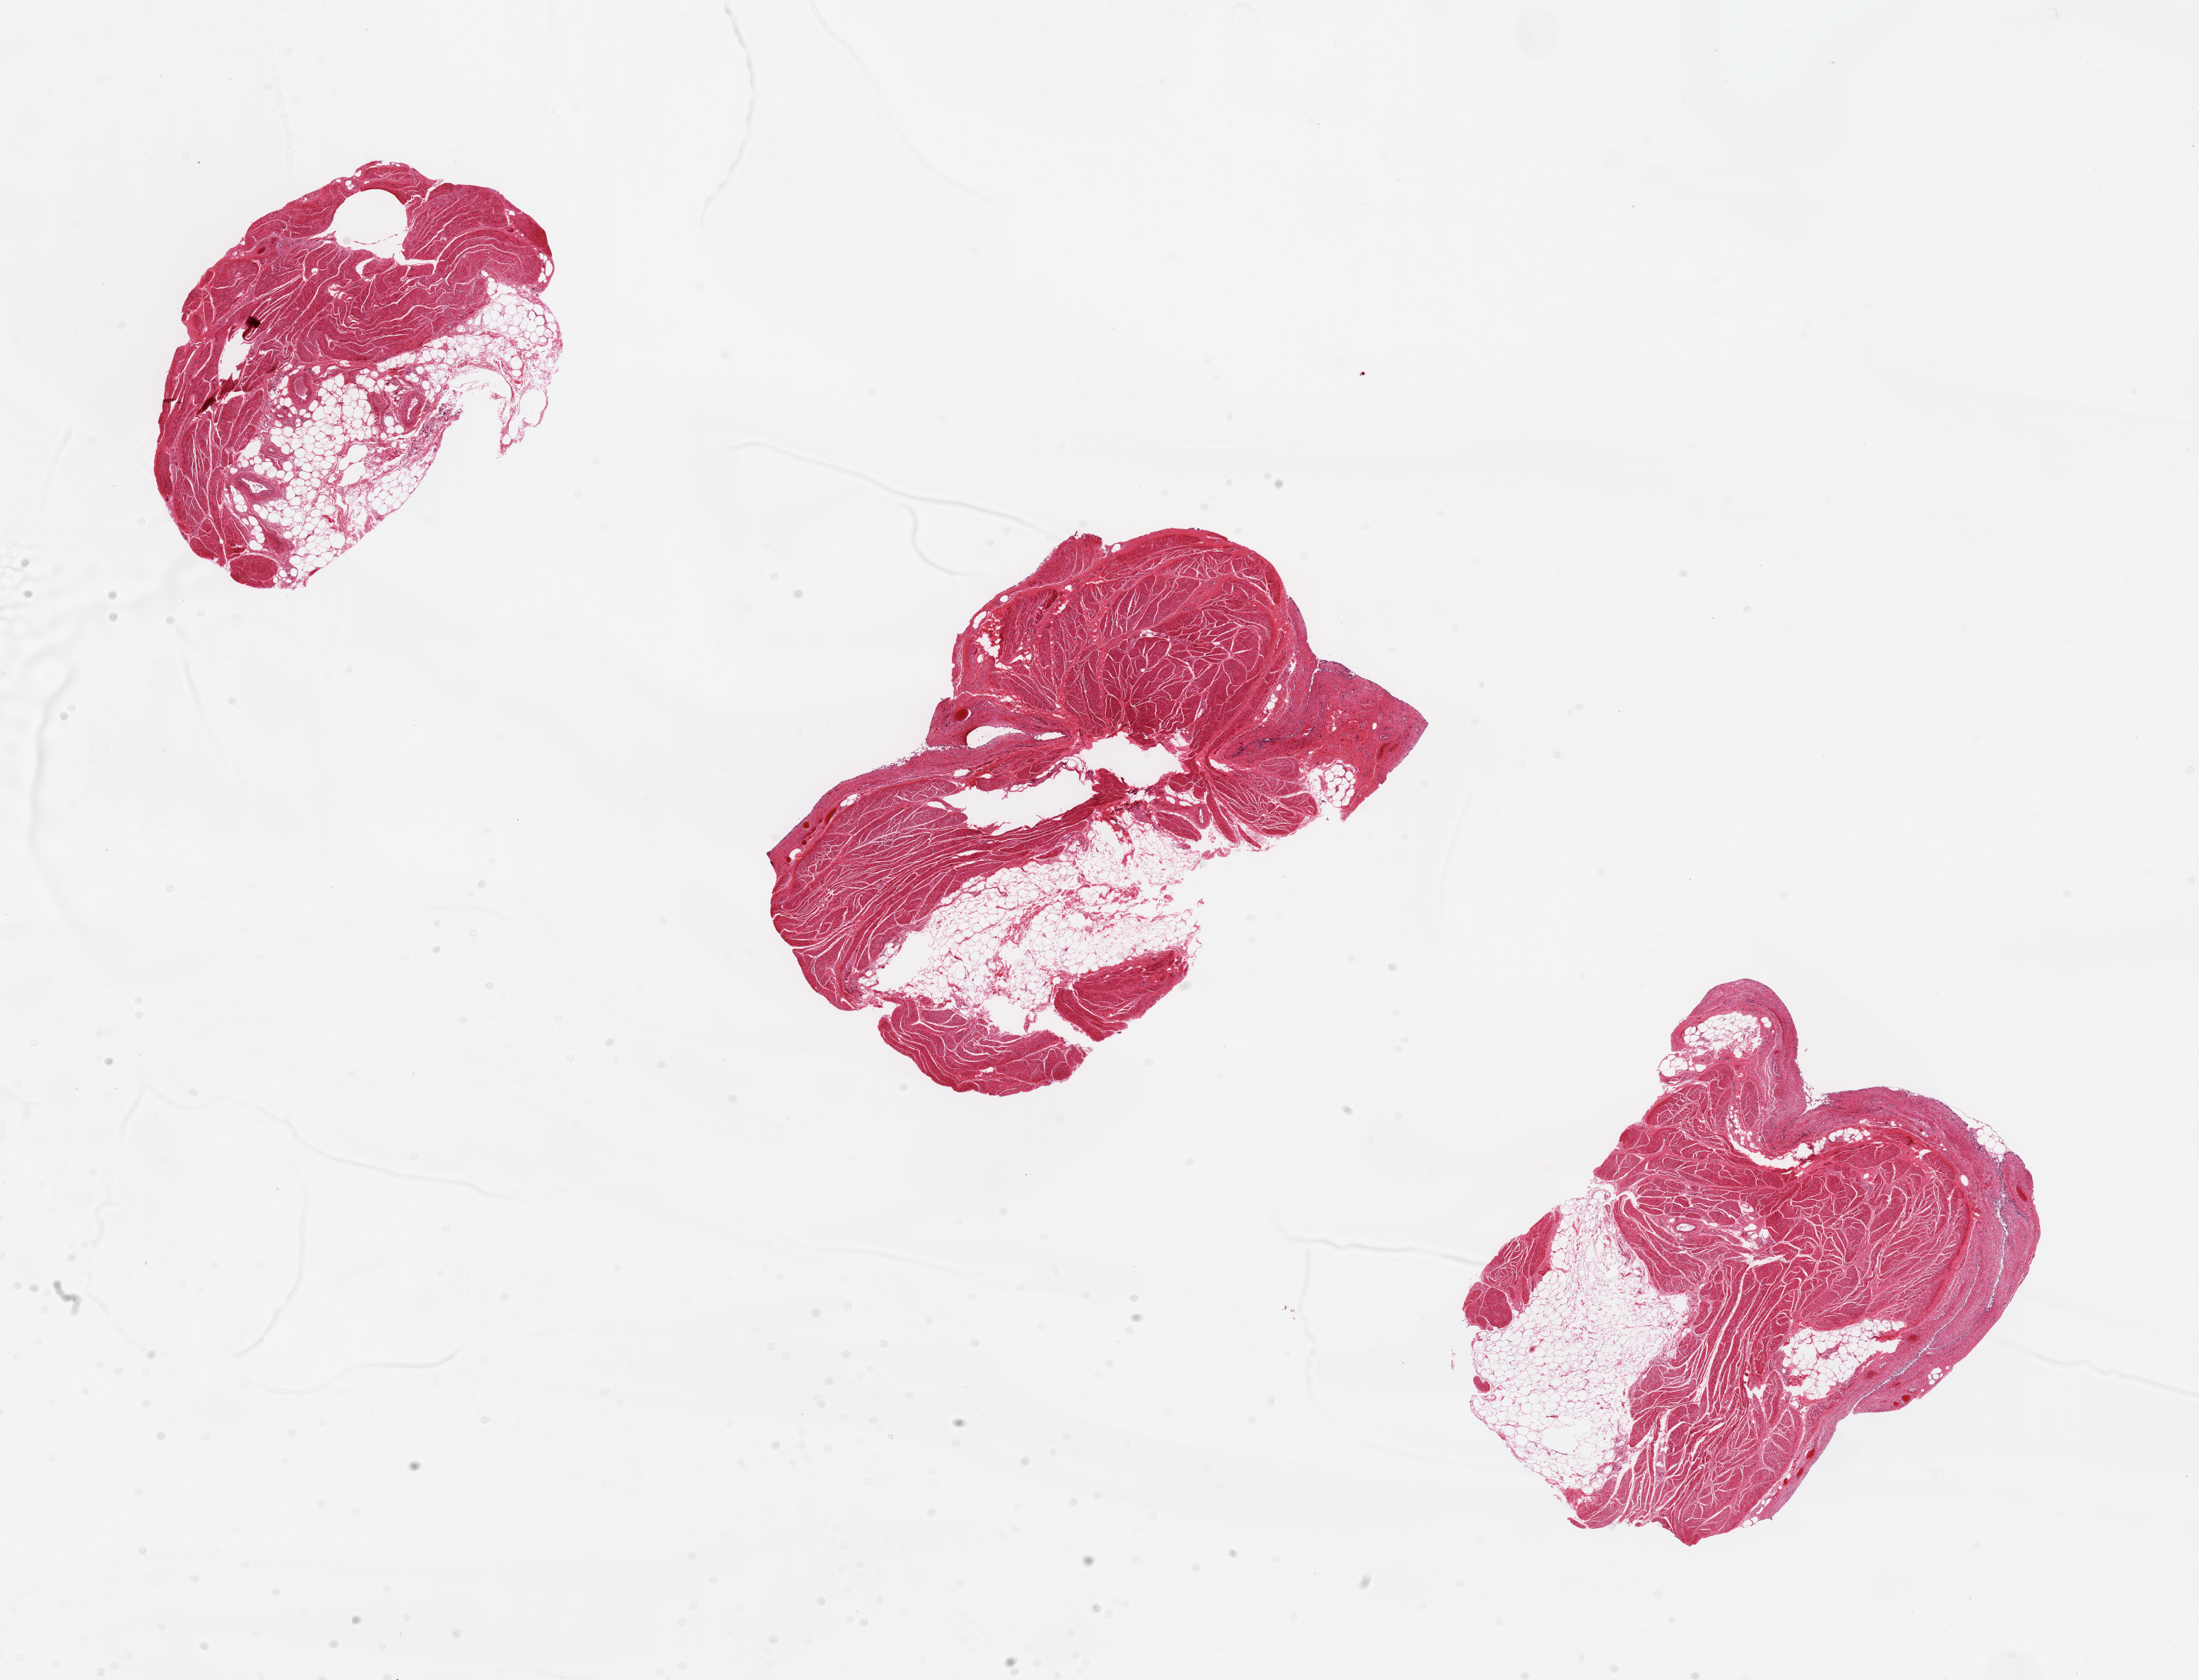
Whole-slide image, haematoxylin and eosin stain, brightfield, a low-resolution overview of the entire scanned area, about 24.6 x 18.8 mm. PAXgene-fixed, paraffin-embedded tissue. Target tissue: urinary bladder. Tissue donor sample. Donor sex: male.
Pathologist's review note for this sample: Mucosa totally sloughed.